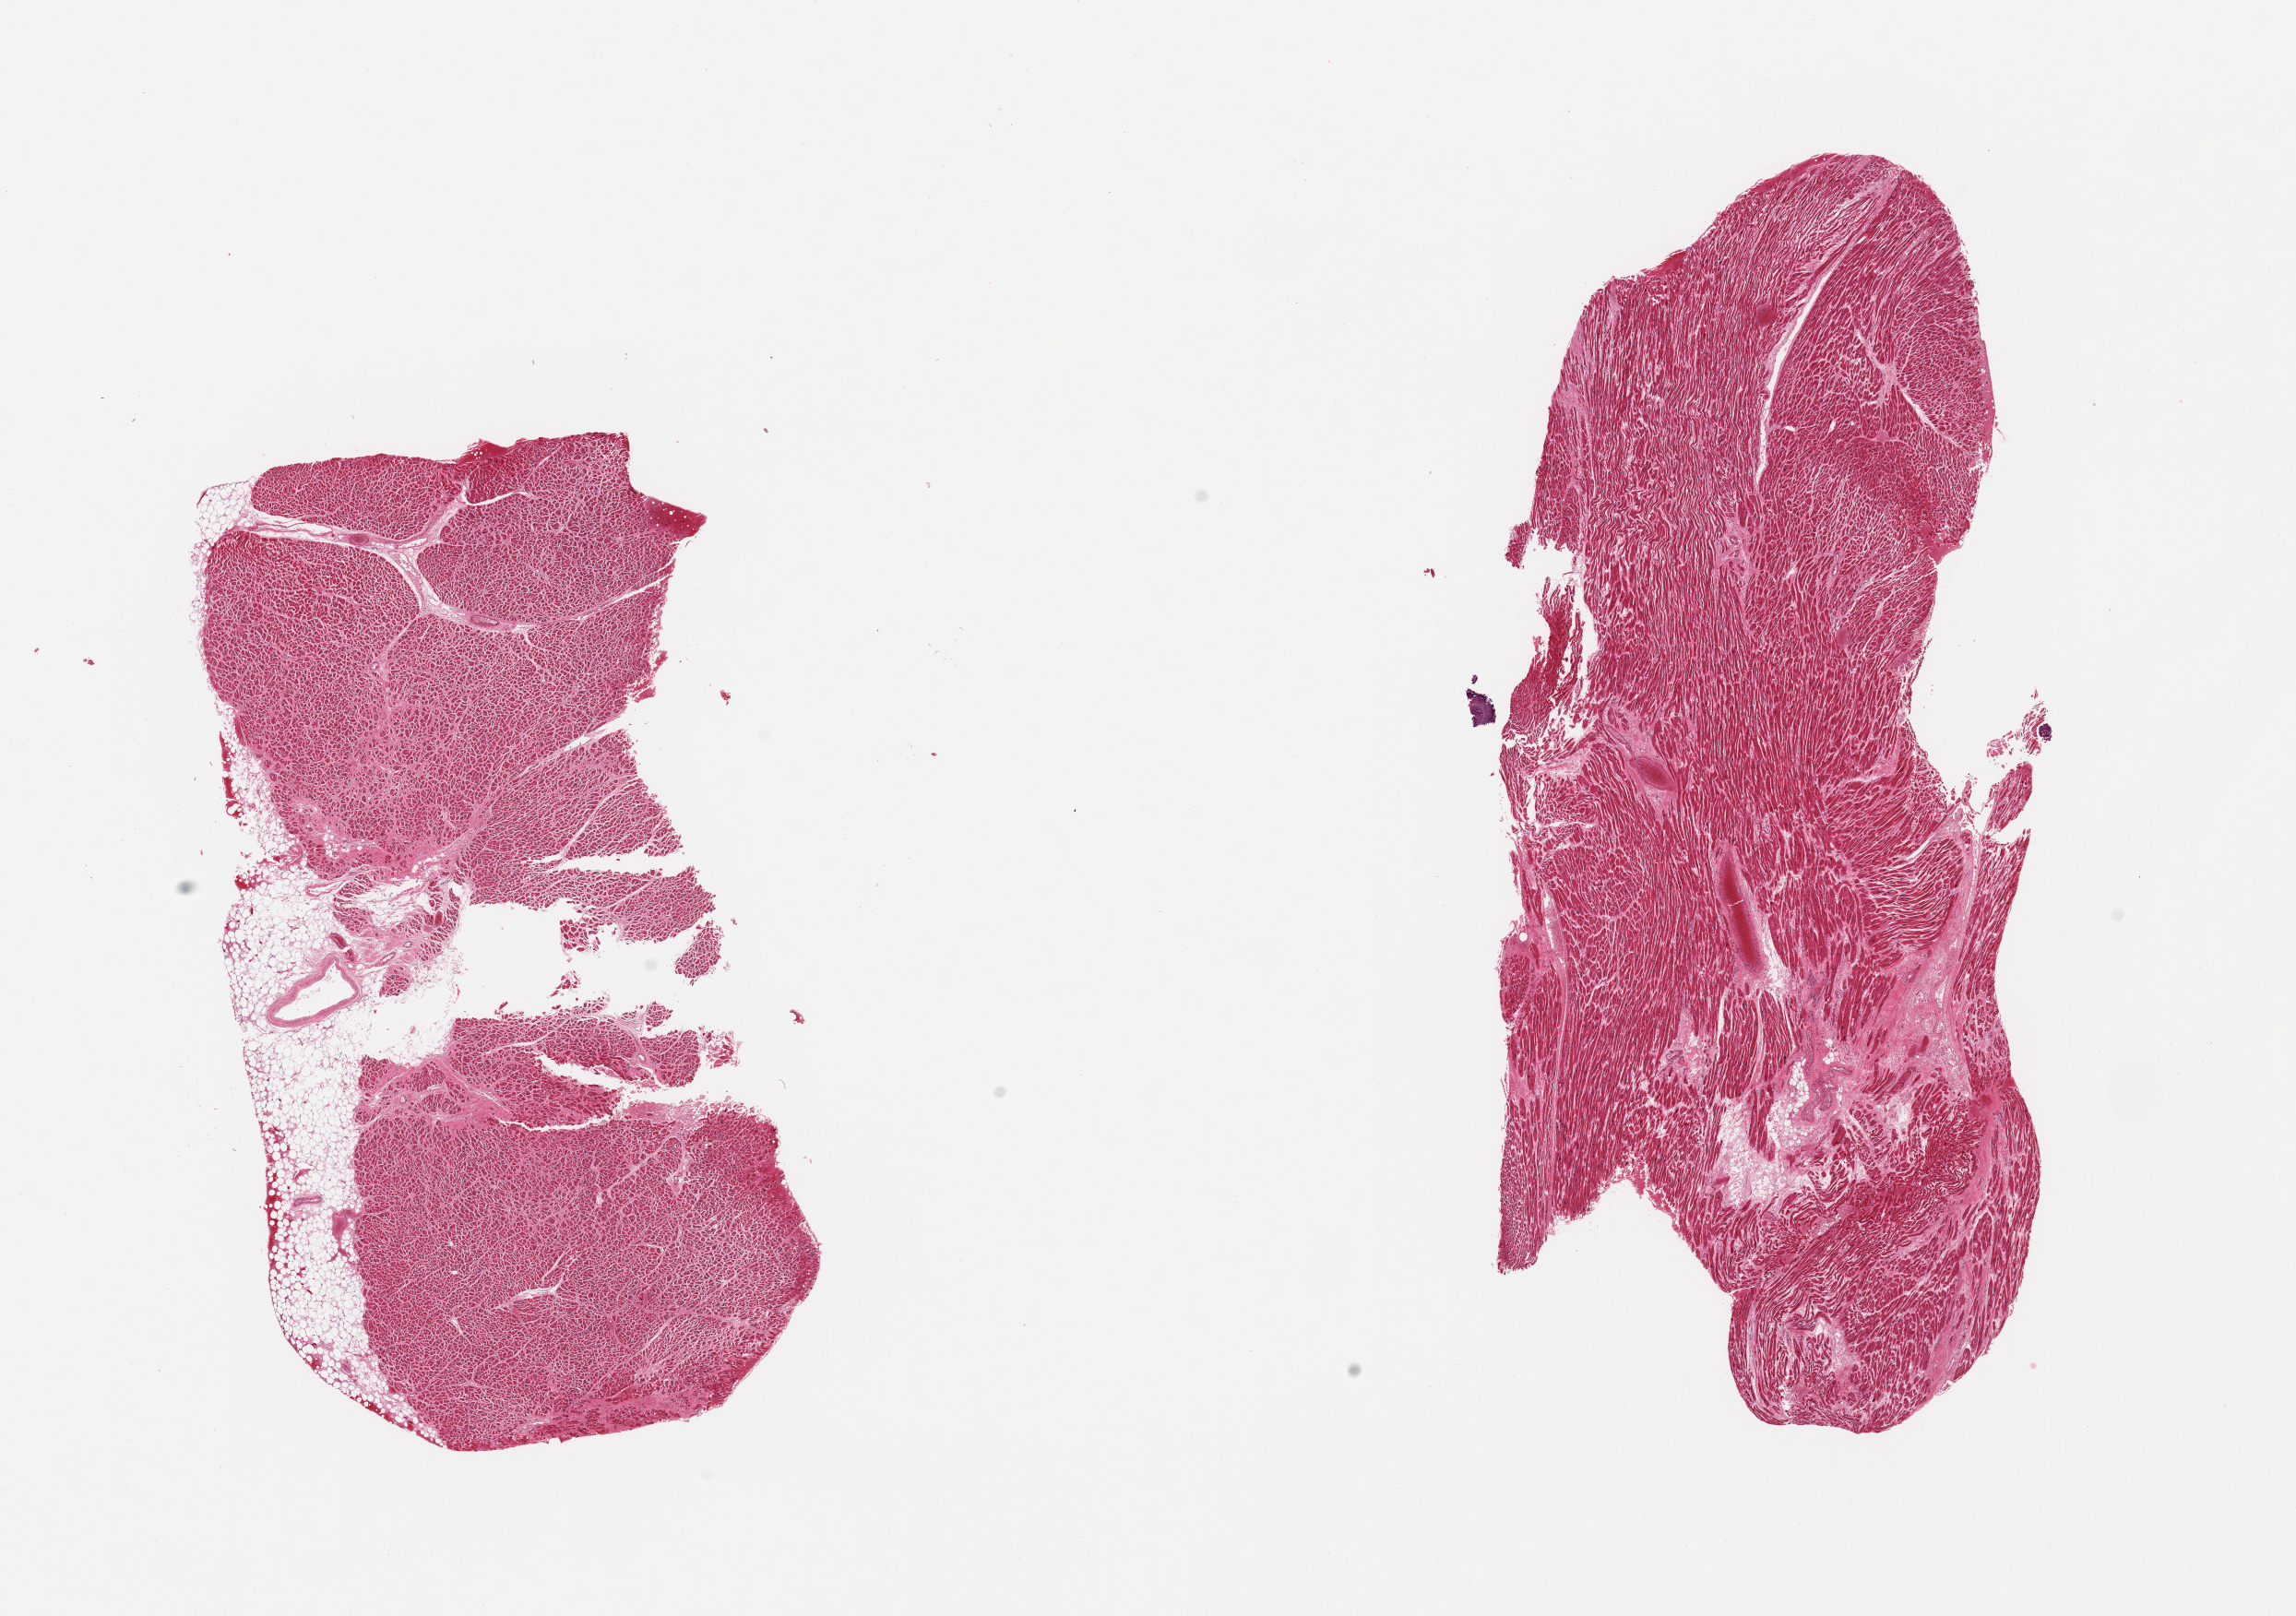
Whole-slide image, H&E stain, whole scanned area (about 19.7 x 13.9 mm, acquisition: 20x scan) shown as a low-resolution overview, PAXgene-fixed paraffin-embedded (PFPE) section, sampled site (target tissue): heart, tissue donor sample. Male donor.
Review note (as recorded): 2 pieces; patchy fibrosis, <5%; 15% pericardial fat on 1 piece.